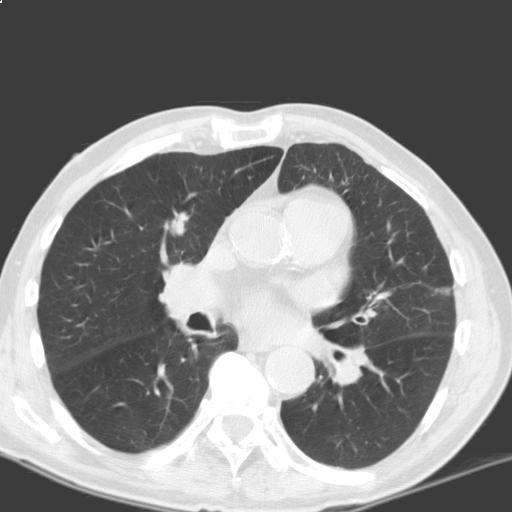
Low-dose screening chest CT, axial slice; baseline annual screen; lung window (W 1500 / L -600 HU); 3.2 mm slice thickness; standard (soft-tissue) reconstruction kernel (C); 120 kVp; slice 88 of 184 in the series. Male participant, aged 69 years at enrolment. Current smoker at enrolment.
Expert reader's lesion annotation, box from (x=150, y=199) to (x=206, y=252) px. The exam's reader record, not a measurement of the box and not confirmed to be the same lesion: non-calcified nodule or mass ≥4 mm, left lower lobe, 5 × 5 mm, smooth margins, soft tissue attenuation. Note: the box lies in the patient's right hemithorax on this image, whereas the reader's record names the left lung; they may be different findings. Later outcome: lung cancer diagnosed 317 days after this screen (after the second annual screen) — squamous cell carcinoma, NOS, right upper lobe, moderately differentiated (G2), stage IB (AJCC 6th edition), 40 mm at pathology.